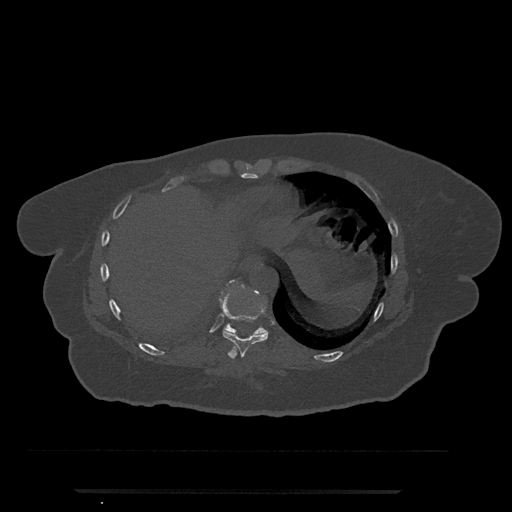
CT including the spine, one axial slice. Slice 324 of 797 in the series (ordered by position). Reconstruction kernel Br40s/3. Bone window (W 1800 / L 400 HU). 512 × 512 image matrix, field of view 440 × 440 mm. Female patient, age 51 years. Case-level facts recorded for this patient, not image findings: primary cancer: neuro; vertebrae with lytic lesions (as recorded): T8.
Structures marked on this image (semi-automatic segmentation, software-assisted and operator-edited):
- T10 vertebra: bounding box (x1, y1, x2, y2) in pixels: (223, 280, 265, 336)
- T9 vertebra: (222, 292, 268, 358)